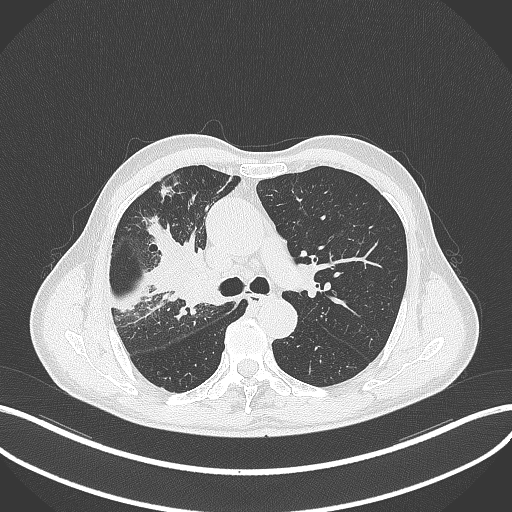
Chest CT, one axial slice; position 318 of 490 along the scan axis; 120 kVp; lung window (W 1500 / L -600 HU); 512 × 512 image matrix. Patient: male, 69 years. Case-level facts recorded for this patient, not image findings: clinical TNM (as recorded): T2a N0 M0.
Annotated regions visible in this slice (rectangle marked by the reading radiologist):
- lung tumour (recorded histology: adenocarcinoma): bounding box <169,248,219,311> (left, top, right, bottom; pixels)